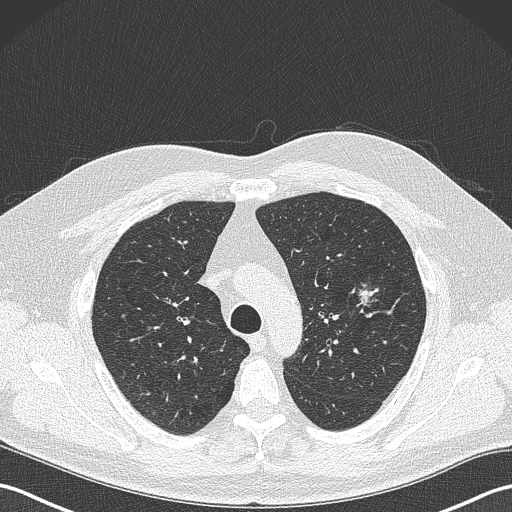
Low-dose screening chest CT, one axial slice; slice 254 of 343 in the series (ordered by position); reconstruction kernel B50f; 120 kVp; lung window (W 1500 / L -600 HU); 512 × 512 image matrix.
Annotated regions visible in this slice (expert manual segmentation):
- lesion 1 (tumor, upper lobe of left lung): box from (x=357, y=287) to (x=373, y=310) px